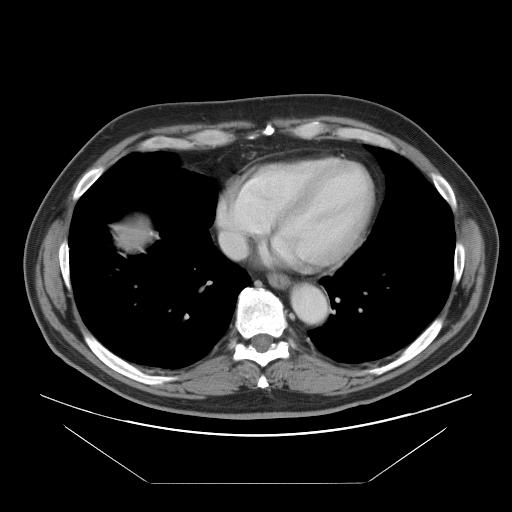
Contrast-enhanced abdominal CT, one axial slice. Slice 92 of 97 in the series (ordered by position). 120 kVp. Intravenous contrast given. Soft-tissue window (W 400 / L 40 HU). 5 mm slice thickness. 512 × 512 image matrix, field of view 442 × 442 mm. Male patient, age 62 years. From the clinical record (not read from this slice): diagnosis: colorectal cancer liver metastases, imaged before liver resection; multiple liver metastases: no; largest metastasis: 7 cm; disease in both lobes: yes.
Structures marked on this image (expert manual segmentation):
- hepatic veins: bounding box [x1, y1, x2, y2] px = [219, 195, 247, 259]